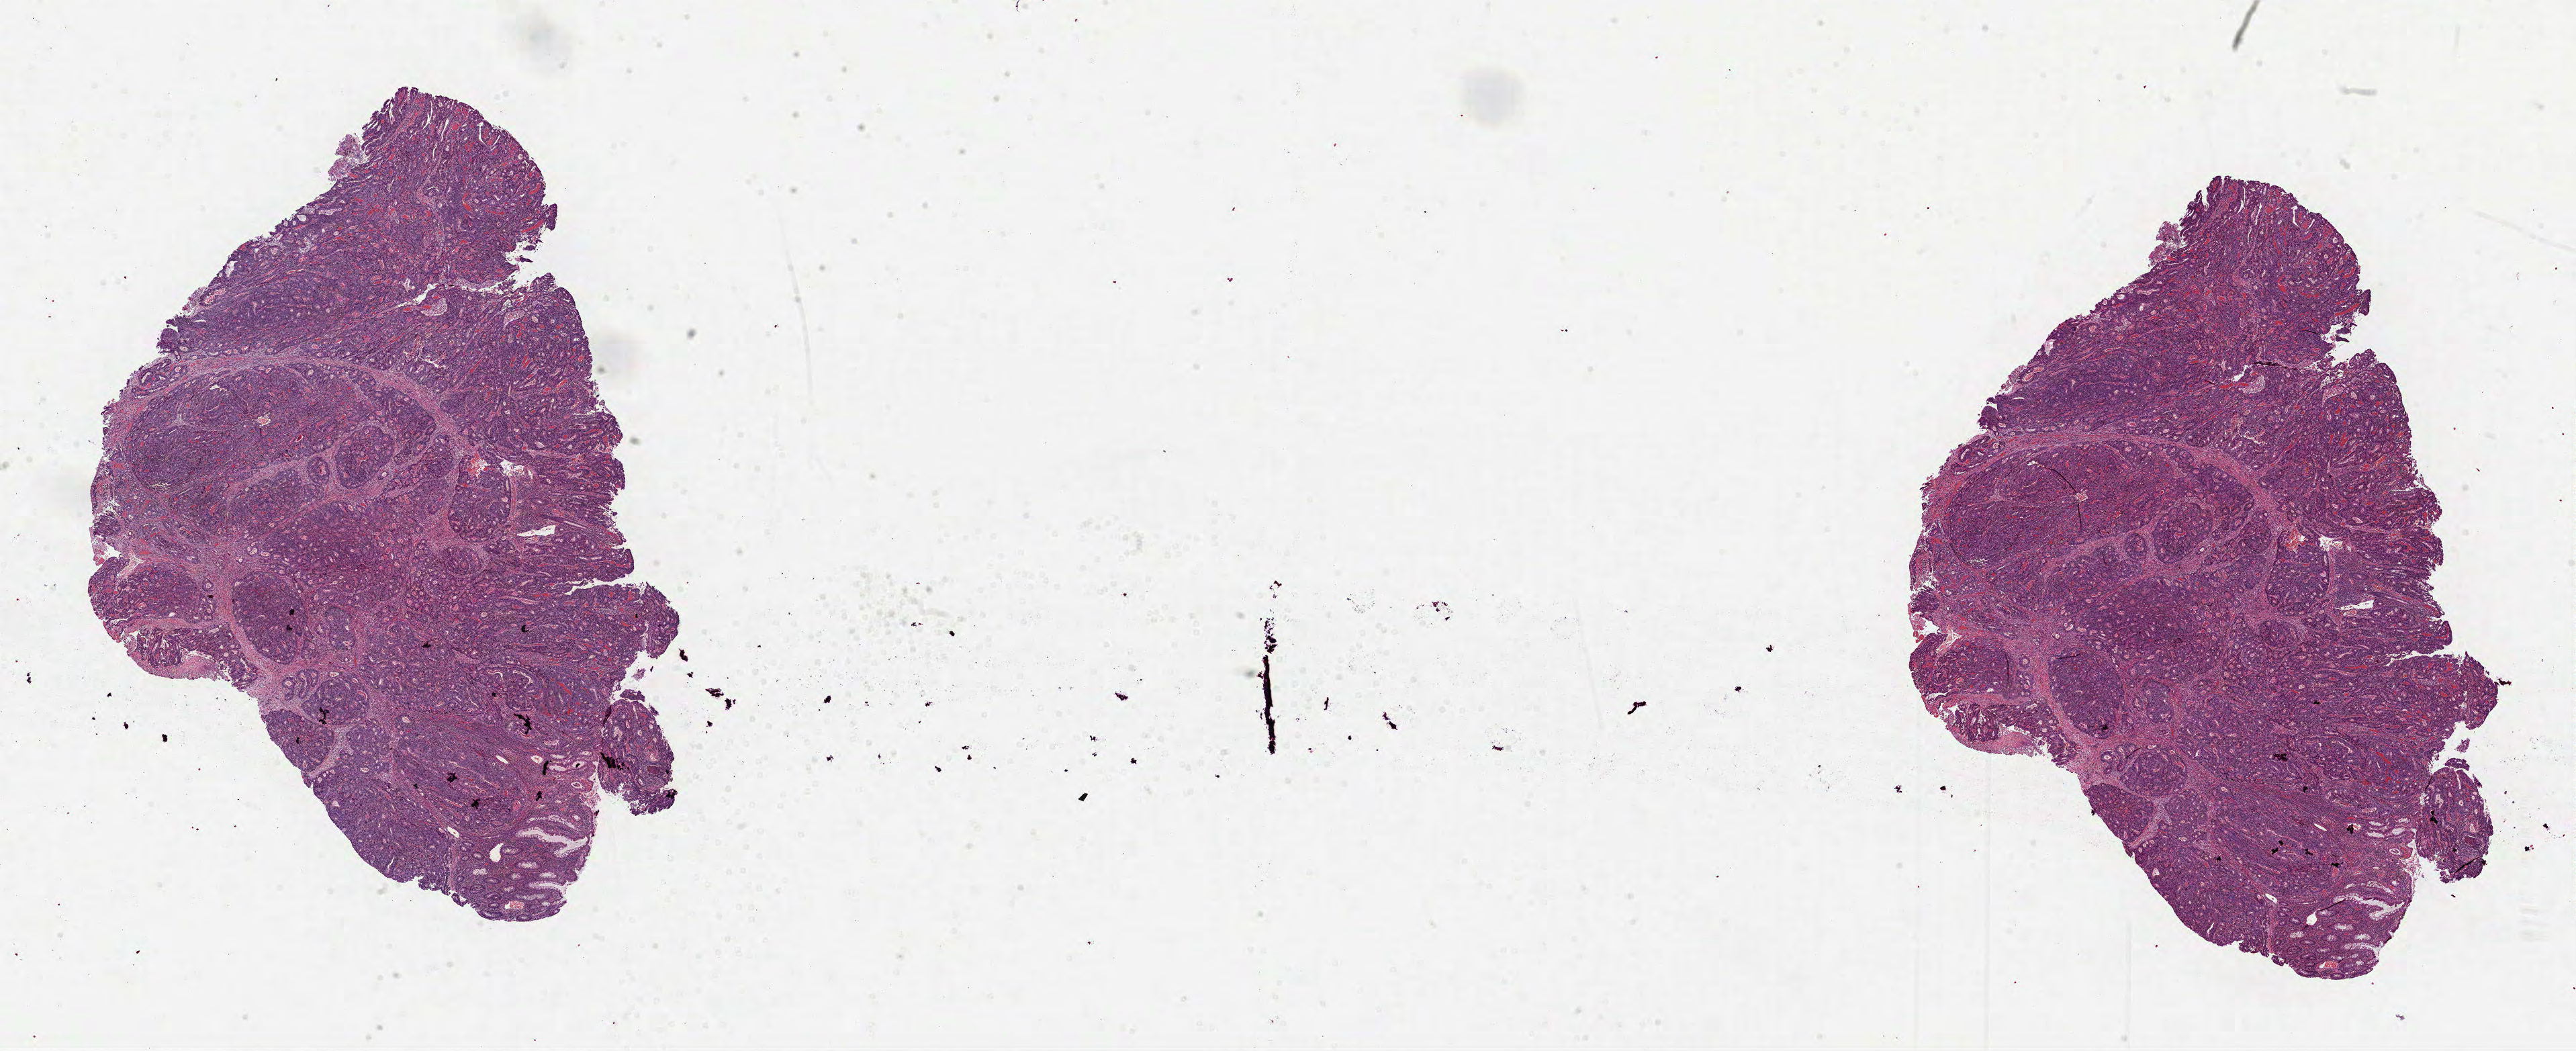
Whole-slide histology image, H&E, a low-resolution overview of the entire scanned area, about 30.9 x 12.6 mm; FFPE section; sample: primary tumour, rectum. Male, age 77 years at initial diagnosis.
* AJCC pathologic stage: IVA
* lymph nodes positive (case pathology): 21 of 34 examined
* diagnosis: Adenocarcinoma, NOS